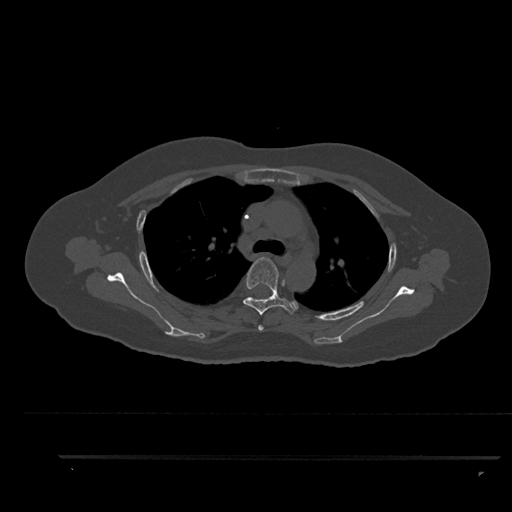
CT including the spine, one axial slice. Slice 644 of 797 in the series (ordered by position). Bone window (W 1800 / L 400 HU). 512 × 512 image matrix, field of view 408 × 408 mm. Patient: female, 44 years. From the clinical record (not read from this slice): primary cancer: renal; vertebrae with lytic lesions (as recorded): L1.
Outlined on this slice (semi-automatic segmentation, software-assisted and operator-edited):
- T3 vertebra: bounding box (x1, y1, x2, y2) in pixels: (258, 325, 264, 331)
- T4 vertebra: (243, 257, 297, 315)